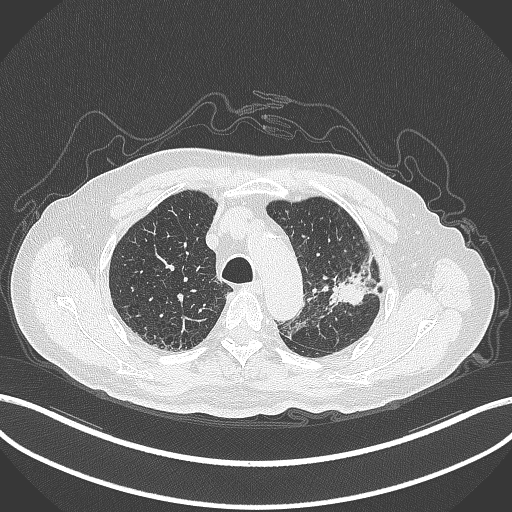
Chest CT, one axial slice; slice 228 of 331 in the series (ordered by position); reconstruction kernel B70f; 120 kVp; lung window (W 1500 / L -600 HU); 1 mm slice thickness; 512 × 512 image matrix, field of view 400 × 400 mm. Patient: male, 79 years. Case-level facts recorded for this patient, not image findings: clinical TNM (as recorded): T2a N1 M1.
Annotated regions visible in this slice (bounding box drawn by a radiologist):
- lung tumour (recorded histology: adenocarcinoma): box from (x=326, y=251) to (x=385, y=309) px